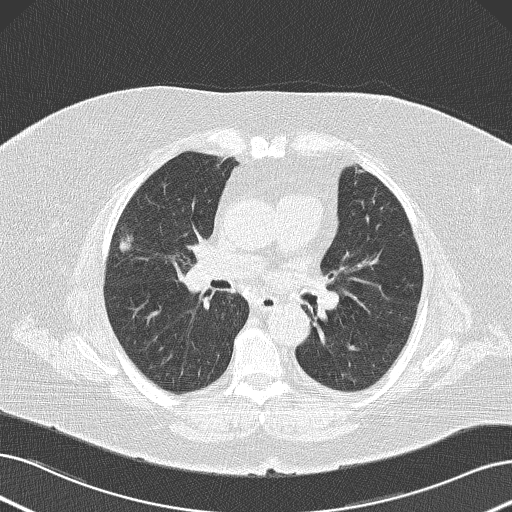
Low-dose screening chest CT, one axial slice. Slice 76 of 145 in the series (ordered by position). Lung window (W 1500 / L -600 HU). 512 × 512 image matrix, field of view 364 × 364 mm.
Outlined on this slice (expert manual segmentation):
- lesion 1 (tumor, upper lobe of right lung): bounding box <119,234,133,253> (left, top, right, bottom; pixels)